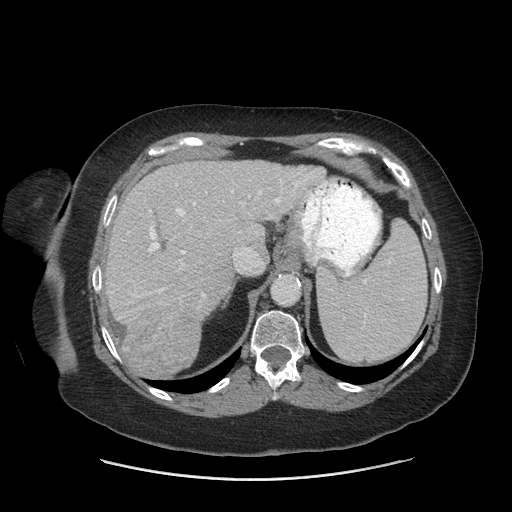
Contrast-enhanced abdominal CT (liver protocol), one axial slice; slice 50 of 69 in the series (ordered by position); reconstruction kernel STANDARD; soft-tissue window (W 400 / L 40 HU); 2.5 mm slice thickness; 512 × 512 image matrix, field of view 420 × 420 mm. From the clinical record (not read from this slice): diagnosis: hepatocellular carcinoma (patient treated with transarterial chemoembolisation; whether this scan precedes or follows treatment is not stated here); TNM stage (as recorded): Stage-IIIB; Child-Pugh class: A.
Outlined on this slice (semi-automatically segmented with operator editing):
- liver parenchyma outside the tumour (the mass and vessels are separate outlines, so this box may not span the whole liver): bounding box [x1, y1, x2, y2] px = [102, 160, 324, 368]
- mass: [122, 303, 200, 378]
- liver vessels: [110, 178, 308, 298]